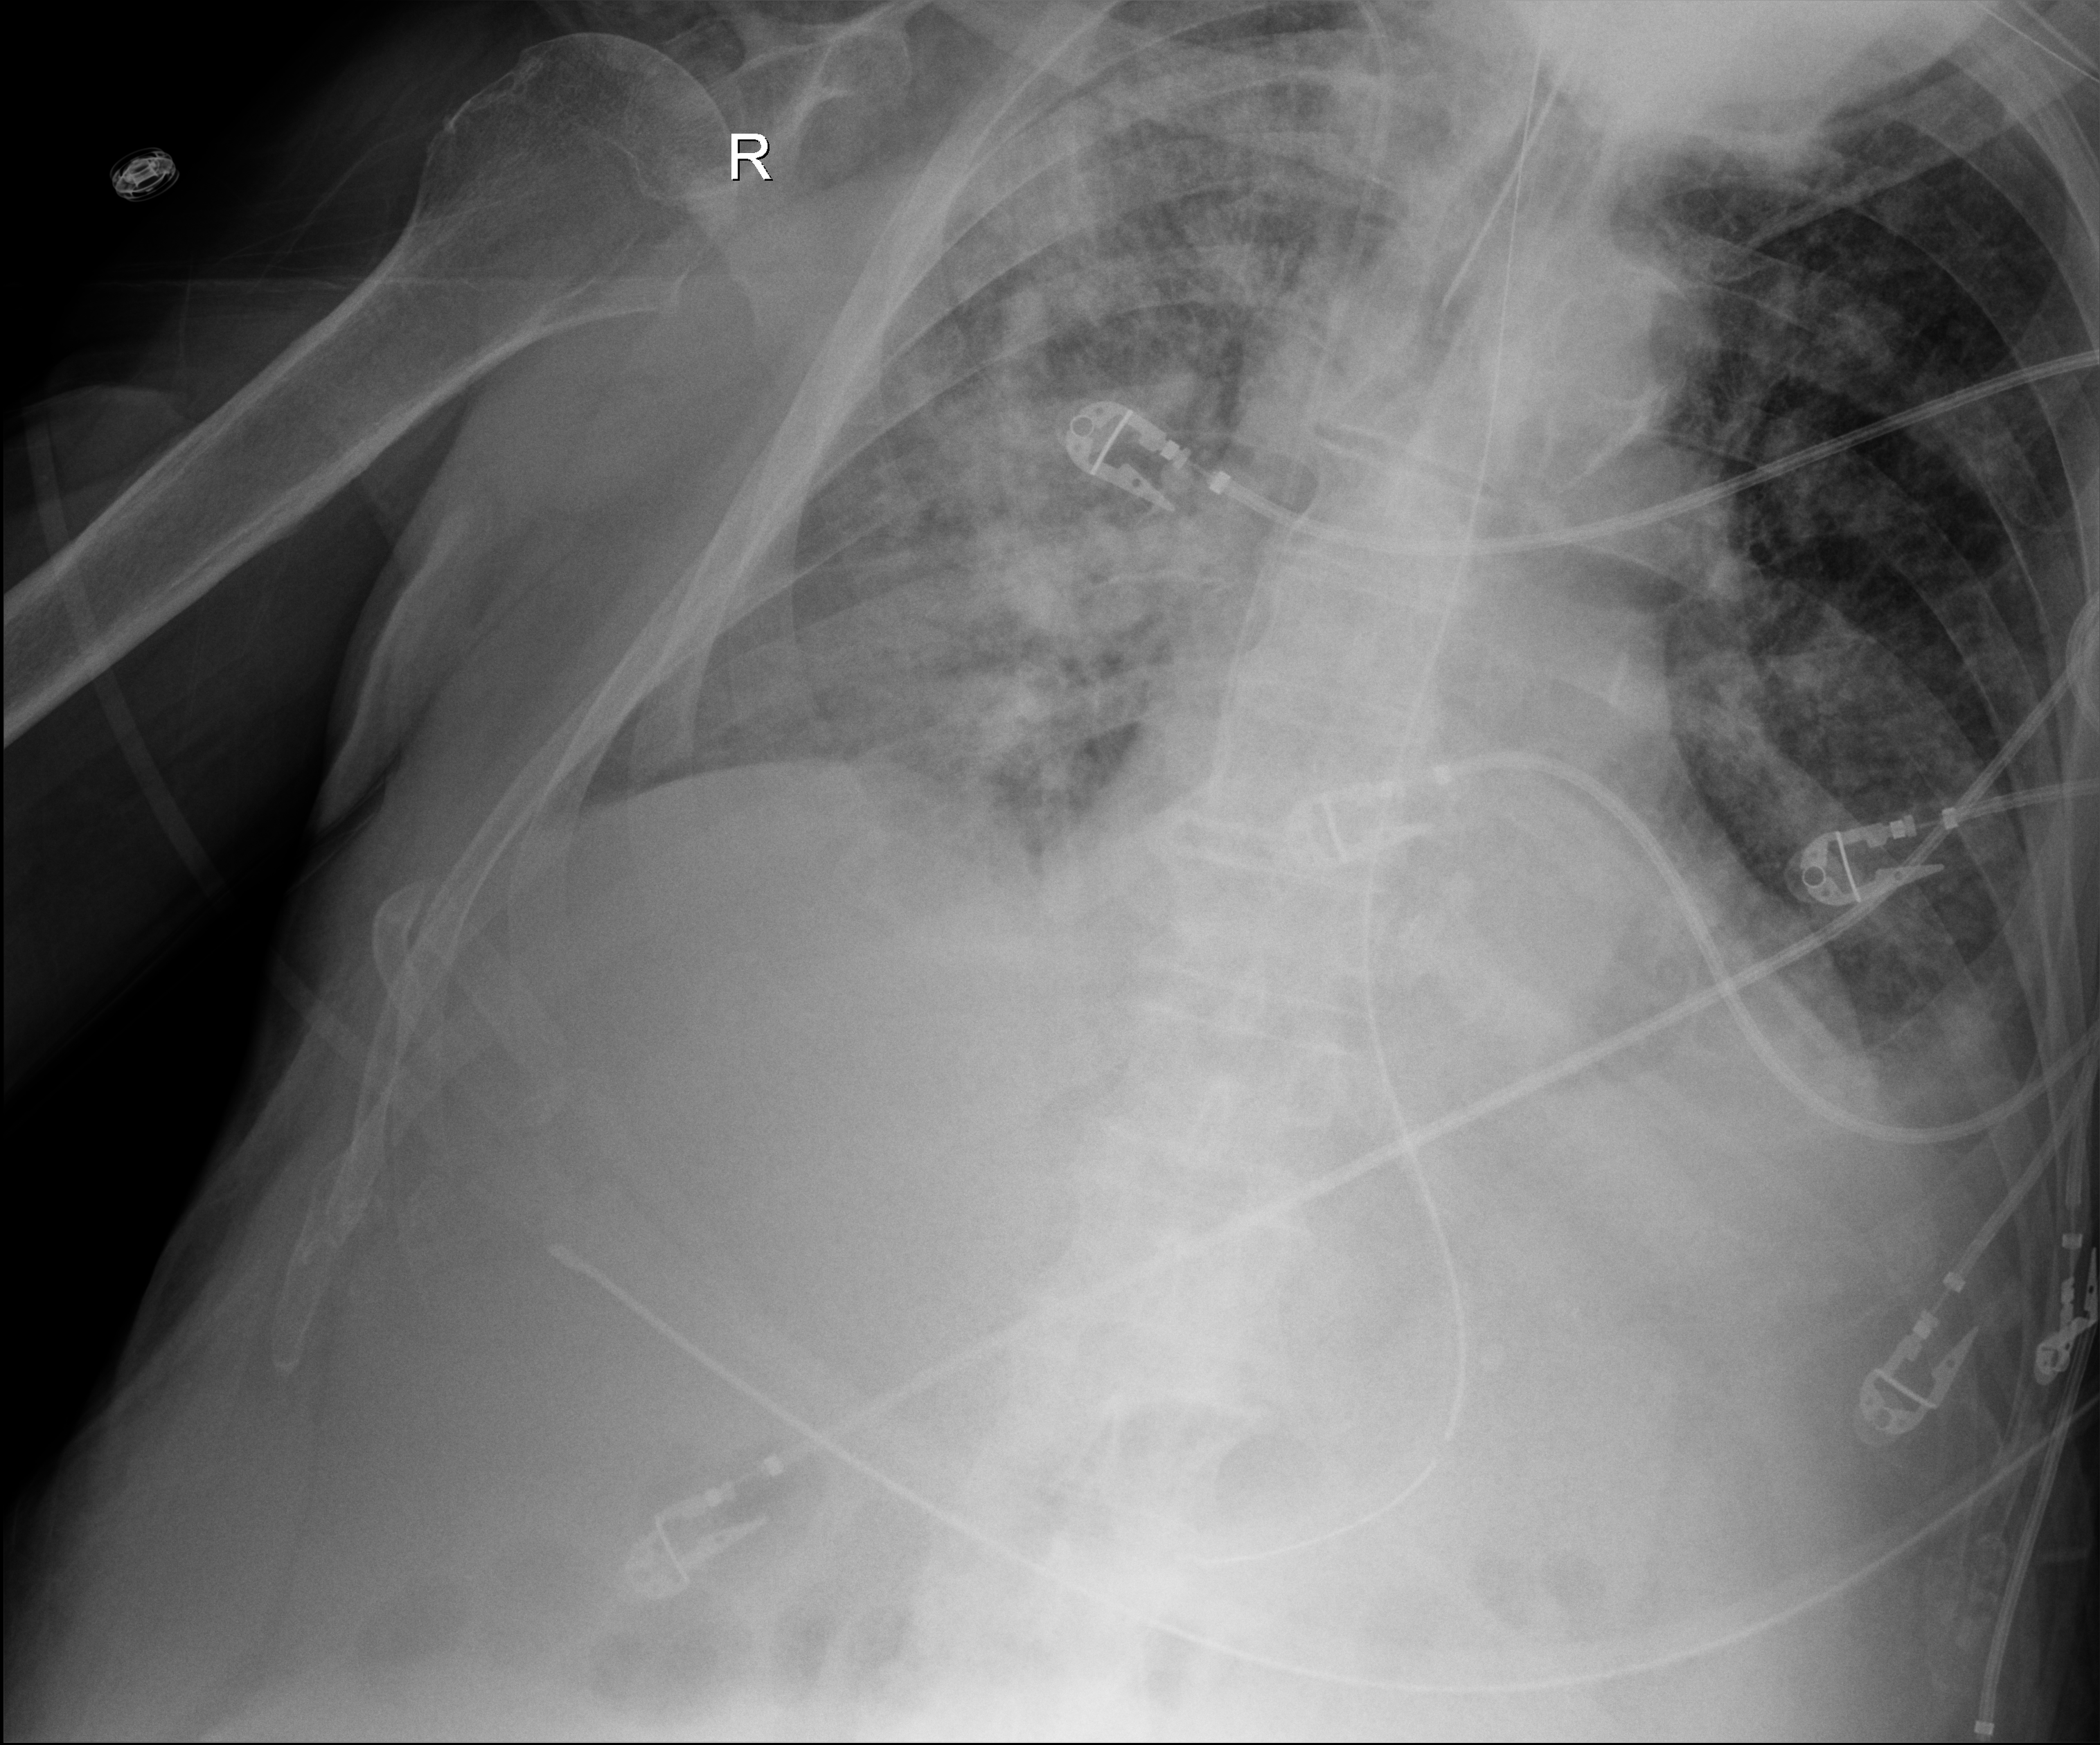
Portable chest radiograph; anteroposterior (AP) projection. Male patient hospitalised with COVID-19, age 75–90 years.
From the hospital-stay record, not from the radiograph (when in the stay this image was taken is not recorded):
- chronic kidney disease (admission record): no
- diabetes (admission record): yes